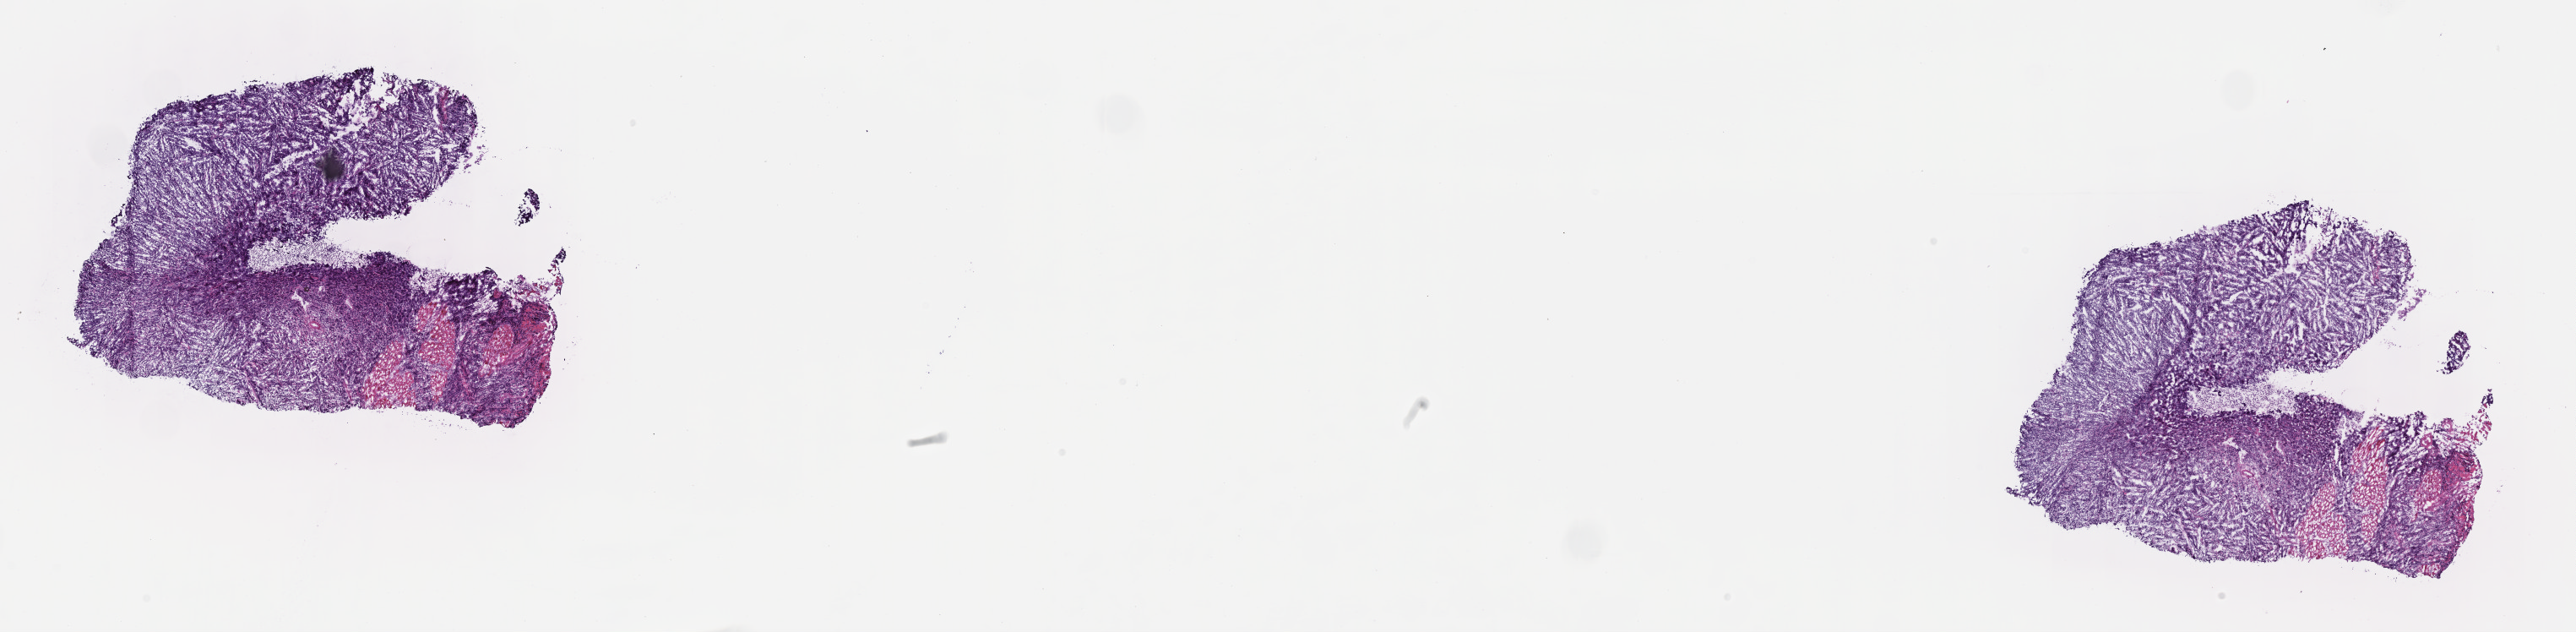
Digitized haematoxylin and eosin-stained section — low-resolution overview of the scanned area, about 24.7 x 6.0 mm, cryosection, specimen: primary tumor, site: cranium. Patient: male, age at initial diagnosis 9 years. Slide review estimates, as recorded: tumor cells 70%, tumor nuclei 80%, stromal cells 30%, necrosis 0%, normal cells 0%. Infiltration values recorded for this section: lymphocyte infiltration 10%, monocyte infiltration 30%, neutrophil infiltration 30%.
• Ann Arbor stage (patient): Stage IV
• histologic diagnosis: Burkitt lymphoma, NOS